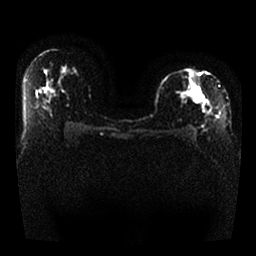
Breast MRI, one axial slice; position 14 of 25 along the scan axis; diffusion-weighted series; image 2 of 4 stored at this slice position (different b-values; order by instance number); 1.5 T; 4 mm slice thickness; 256 × 256 image matrix, field of view 330 × 330 mm. Female patient.
Annotated regions visible in this slice (manually delineated by an expert):
- tumour on diffusion-weighted imaging: bounding box <177,81,213,115> (left, top, right, bottom; pixels)